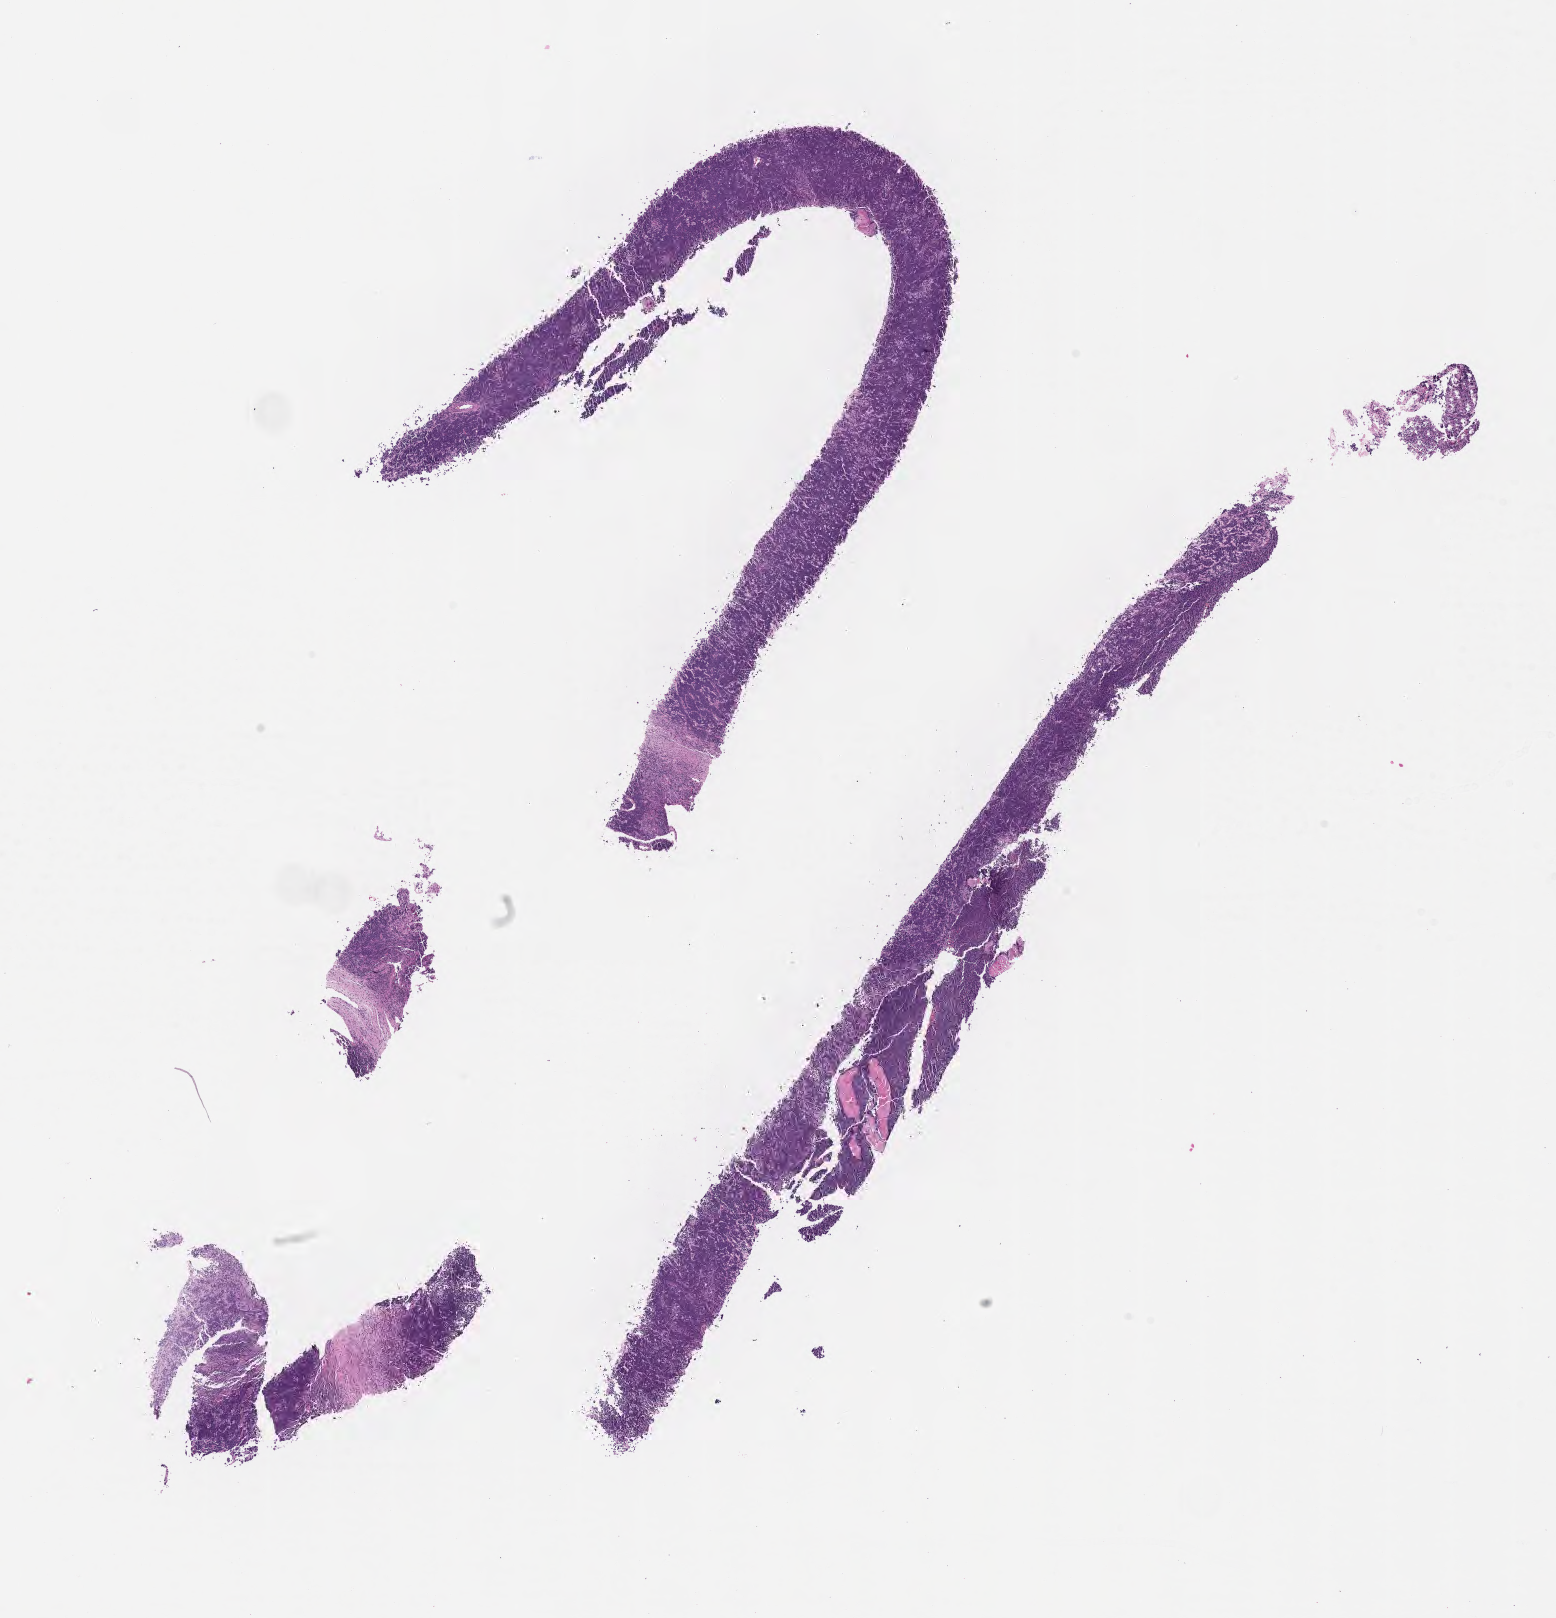
Digitized H&E-stained section — a low-resolution overview of the entire scanned area, about 12.6 x 13.1 mm, FFPE section, specimen: primary tumor. Patient male; aged 55. Composition of this section per pathologist review: tumor cells 90%, tumor nuclei 95%, stromal cells 5%, necrosis 5%, normal cells 0%. Infiltration values recorded for this section: lymphocyte infiltration 50%, monocyte infiltration 20%, neutrophil infiltration 5%.
- diagnosis: Burkitt lymphoma, NOS
- Ann Arbor stage (patient): Stage I